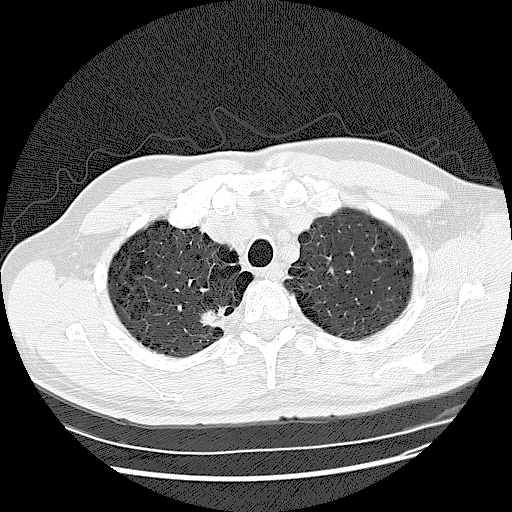
Low-dose screening chest CT, one axial slice. Position 110 of 132 along the scan axis. Reconstruction kernel LUNG. 120 kVp. Lung window (W 1500 / L -600 HU). 512 × 512 image matrix, field of view 380 × 380 mm.
Structures marked on this image (expert manual segmentation):
- lesion 1 (tumor, upper lobe of right lung): box from (x=200, y=306) to (x=225, y=330) px